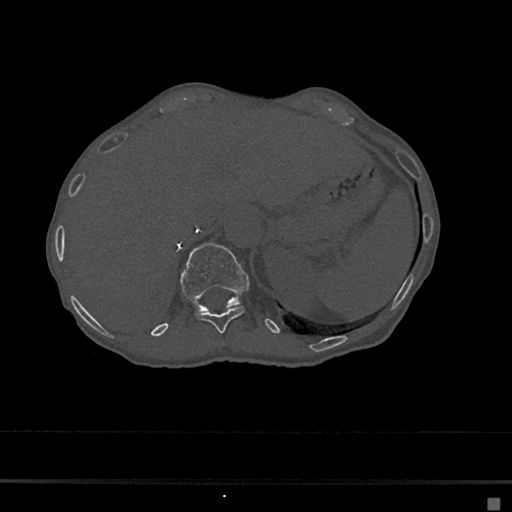
CT including the spine, one axial slice; slice 152 of 797 in the series (ordered by position); reconstruction kernel Br40s/3; 120 kVp; bone window (W 1800 / L 400 HU); 512 × 512 image matrix. Patient: female, 68 years. From the clinical record (not read from this slice): primary cancer: renal.
Outlined on this slice (semi-automatic segmentation, software-assisted and operator-edited):
- T11 vertebra: bounding box (x1, y1, x2, y2) in pixels: (195, 305, 245, 334)
- T12 vertebra: (180, 243, 249, 312)